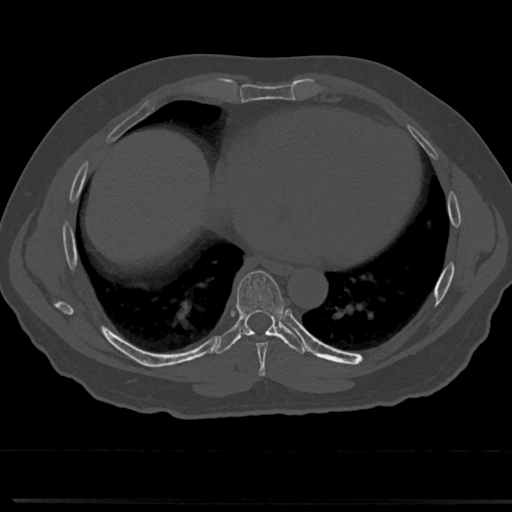
CT including the spine, one axial slice; slice 369 of 817 in the series (ordered by position); 120 kVp; bone window (W 1800 / L 400 HU); 0.5 mm slice thickness; 512 × 512 image matrix. Patient: male, 61 years. From the clinical record (not read from this slice): primary cancer: prostate.
Outlined on this slice (semi-automatic segmentation, software-assisted and operator-edited):
- T7 vertebra: box from (x=236, y=272) to (x=287, y=358) px
- T8 vertebra: (x=237, y=324)–(x=282, y=334)